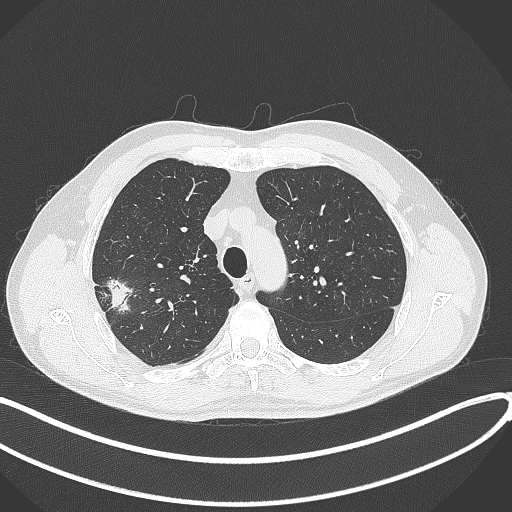
Chest CT, one axial slice; slice 317 of 381 in the series (ordered by position); reconstruction kernel B70f; 120 kVp; lung window (W 1500 / L -600 HU); 1 mm slice thickness; 512 × 512 image matrix, field of view 400 × 400 mm. Male patient, age 62 years. From the clinical record (not read from this slice): clinical TNM (as recorded): T1c N0 M0; histopathological grade: G2-3.
Annotated regions visible in this slice (bounding box drawn by a radiologist):
- lung tumour (recorded histology: adenocarcinoma): box from (x=104, y=269) to (x=134, y=313) px